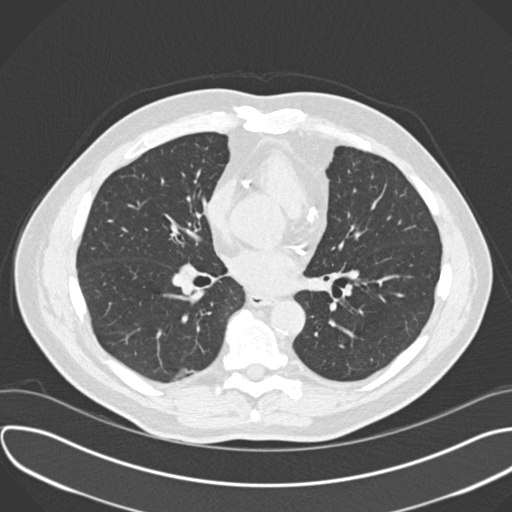
Chest CT (low-dose screening protocol), one axial image; baseline screening round; lung window (W 1500 / L -600 HU); 2 mm slice thickness; 120 kVp; slice 99 of 205 in the series. Male participant, aged 68 years at enrolment. Former smoker at enrolment.
Expert reader's lesion annotation, bounding box [x1, y1, x2, y2] px = [166, 358, 212, 391]. Screening reader's record for this exam (one nodule recorded; not confirmed to be the boxed lesion): non-calcified nodule or mass ≥4 mm, lingula, 6 × 3 mm, smooth margins, soft tissue attenuation. Note: the box lies in the patient's right hemithorax on this image, whereas the reader's record names the left lung; they may be different findings. Official screen result: positive, change unspecified: nodule(s) >= 4 mm or enlarging nodule(s), mass(es), or other non-specific abnormalities suspicious for lung cancer. Lung cancer was diagnosed 817 days after this screen: adenosquamous carcinoma, right lower lobe, moderately differentiated (G2), stage IB (AJCC 6th edition), 31 mm at pathology.